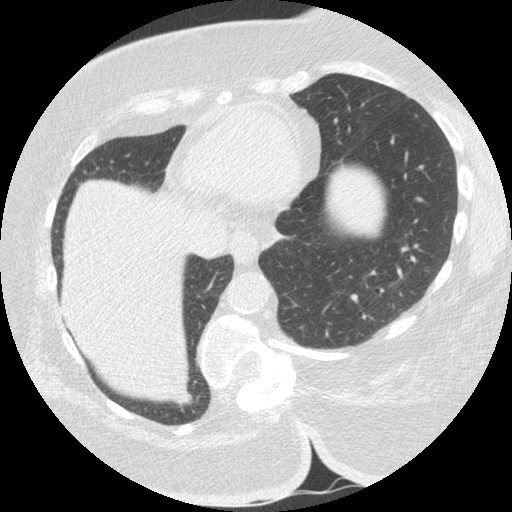
Low-dose screening chest CT, one axial slice. Slice 45 of 151 in the series (ordered by position). Lung window (W 1500 / L -600 HU). 512 × 512 image matrix, field of view 340 × 340 mm.
Structures marked on this image (manually delineated by an expert):
- lesion 1 (tumor, lower lobe of right lung): bounding box <179,394,197,411> (left, top, right, bottom; pixels)